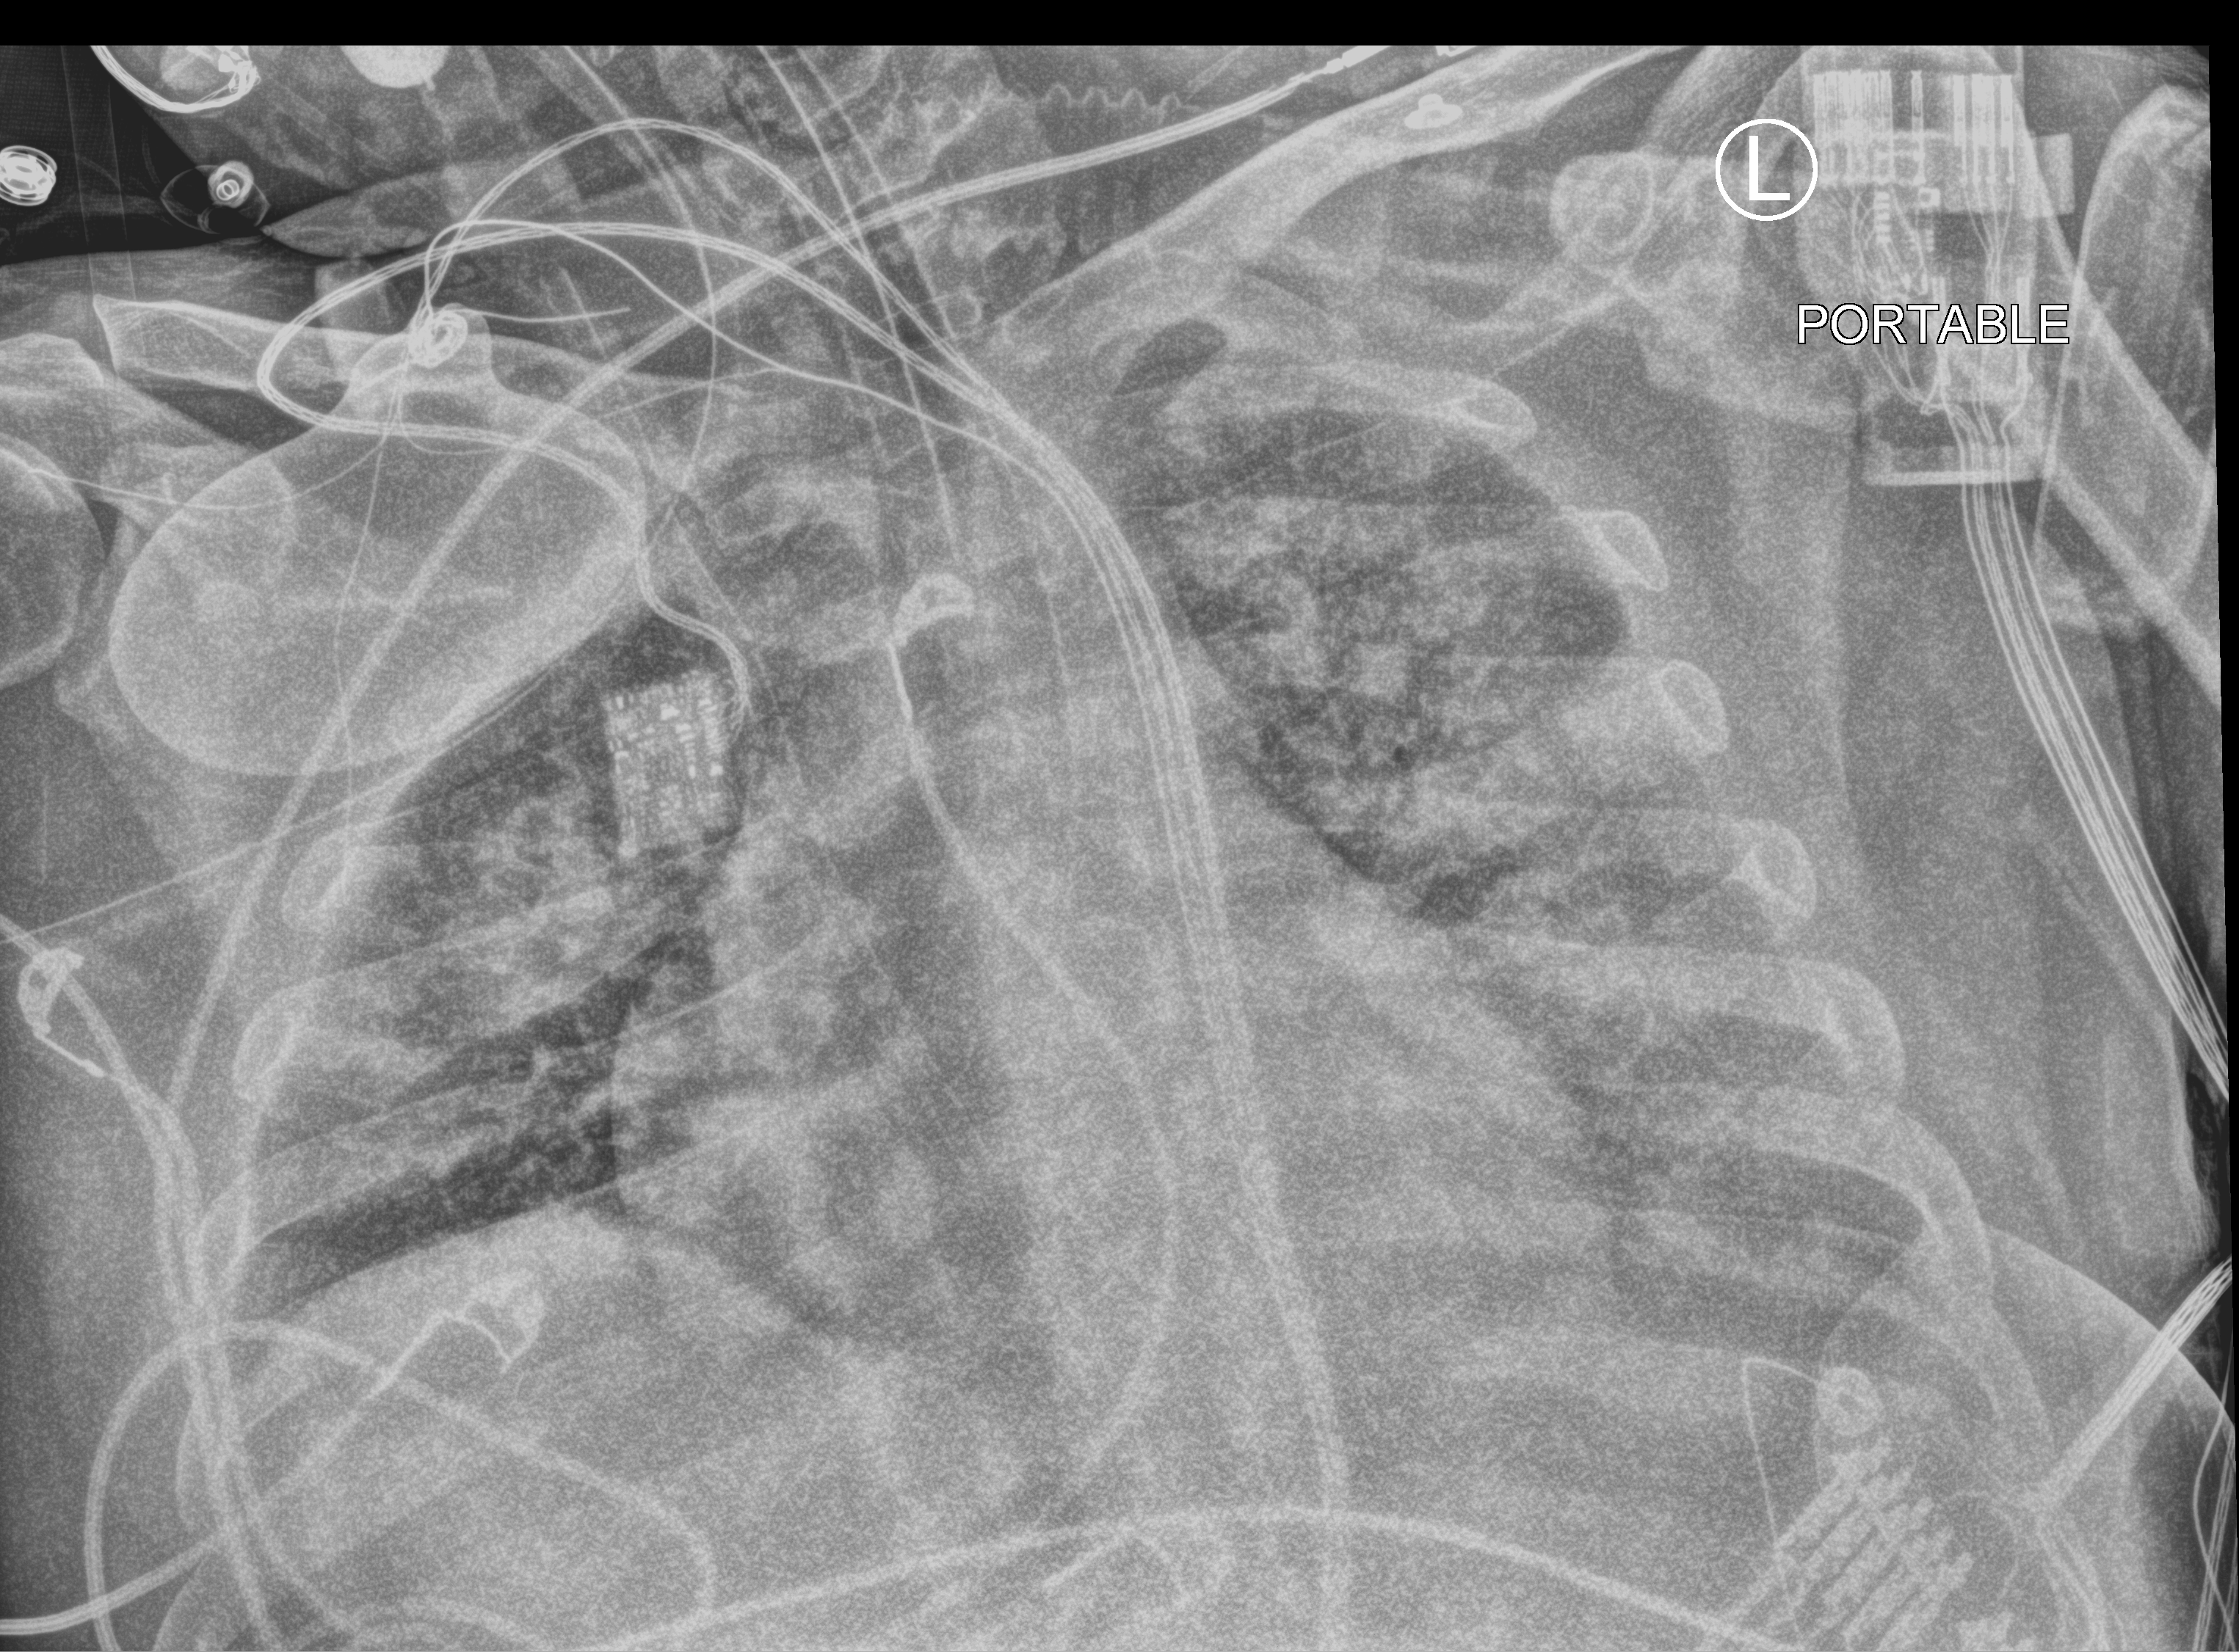
Chest X-ray (portable). Patient hospitalised with COVID-19; male, aged 18–59 years.
From the hospital-stay record, not from the radiograph (when in the stay this image was taken is not recorded):
- COPD (admission record): no